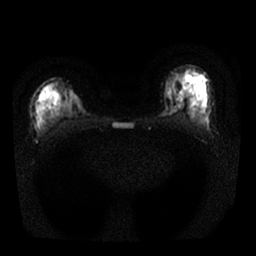
Breast MRI, one axial slice; position 8 of 25 along the scan axis; diffusion-weighted series; image 2 of 4 stored at this slice position (different b-values; order by instance number); 1.5 T; 4 mm slice thickness; 256 × 256 image matrix, field of view 320 × 320 mm. Female patient.
Structures marked on this image (manually delineated by an expert):
- tumour on diffusion-weighted imaging: bounding box (x1, y1, x2, y2) in pixels: (196, 116, 201, 120)